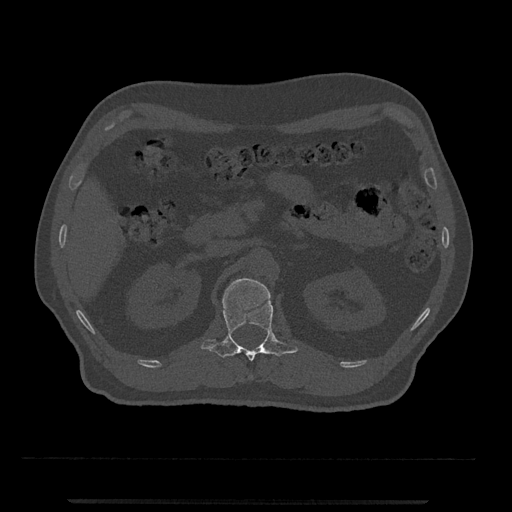
CT including the spine, one axial slice; slice 340 of 797 in the series (ordered by position); 120 kVp; bone window (W 1800 / L 400 HU); 0.5 mm slice thickness; 512 × 512 image matrix, field of view 419 × 419 mm. Patient: male, 63 years. Case-level facts recorded for this patient, not image findings: primary cancer: prostate.
Annotated regions visible in this slice (semi-automatically segmented with operator editing):
- L1 vertebra: bounding box <201,278,298,361> (left, top, right, bottom; pixels)